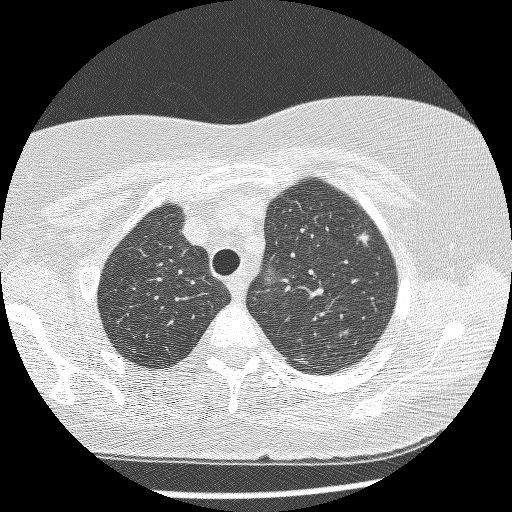
Chest CT (low-dose screening protocol), one axial image; baseline screening round; lung window (W 1500 / L -600 HU); 1.25 mm slice thickness; 120 kVp. Female participant, aged 61 years at enrolment. Current smoker at enrolment.
• Lesion marked by an expert reader, bounding box [x1, y1, x2, y2] px = [330, 221, 385, 271].
• The screening reader recorded 4 non-calcified nodules or masses ≥4 mm on this exam (right lower lobe, right middle lobe, right lower lobe, left upper lobe); which of them this box marks is not recorded.
• Official screen result: positive, change unspecified: nodule(s) >= 4 mm or enlarging nodule(s), mass(es), or other non-specific abnormalities suspicious for lung cancer.
• Participant outcome: lung cancer diagnosed 111 days after this screen — bronchiolo-alveolar adenocarcinoma, NOS, left upper lobe, stage IV (AJCC 6th edition), 10 mm at pathology.